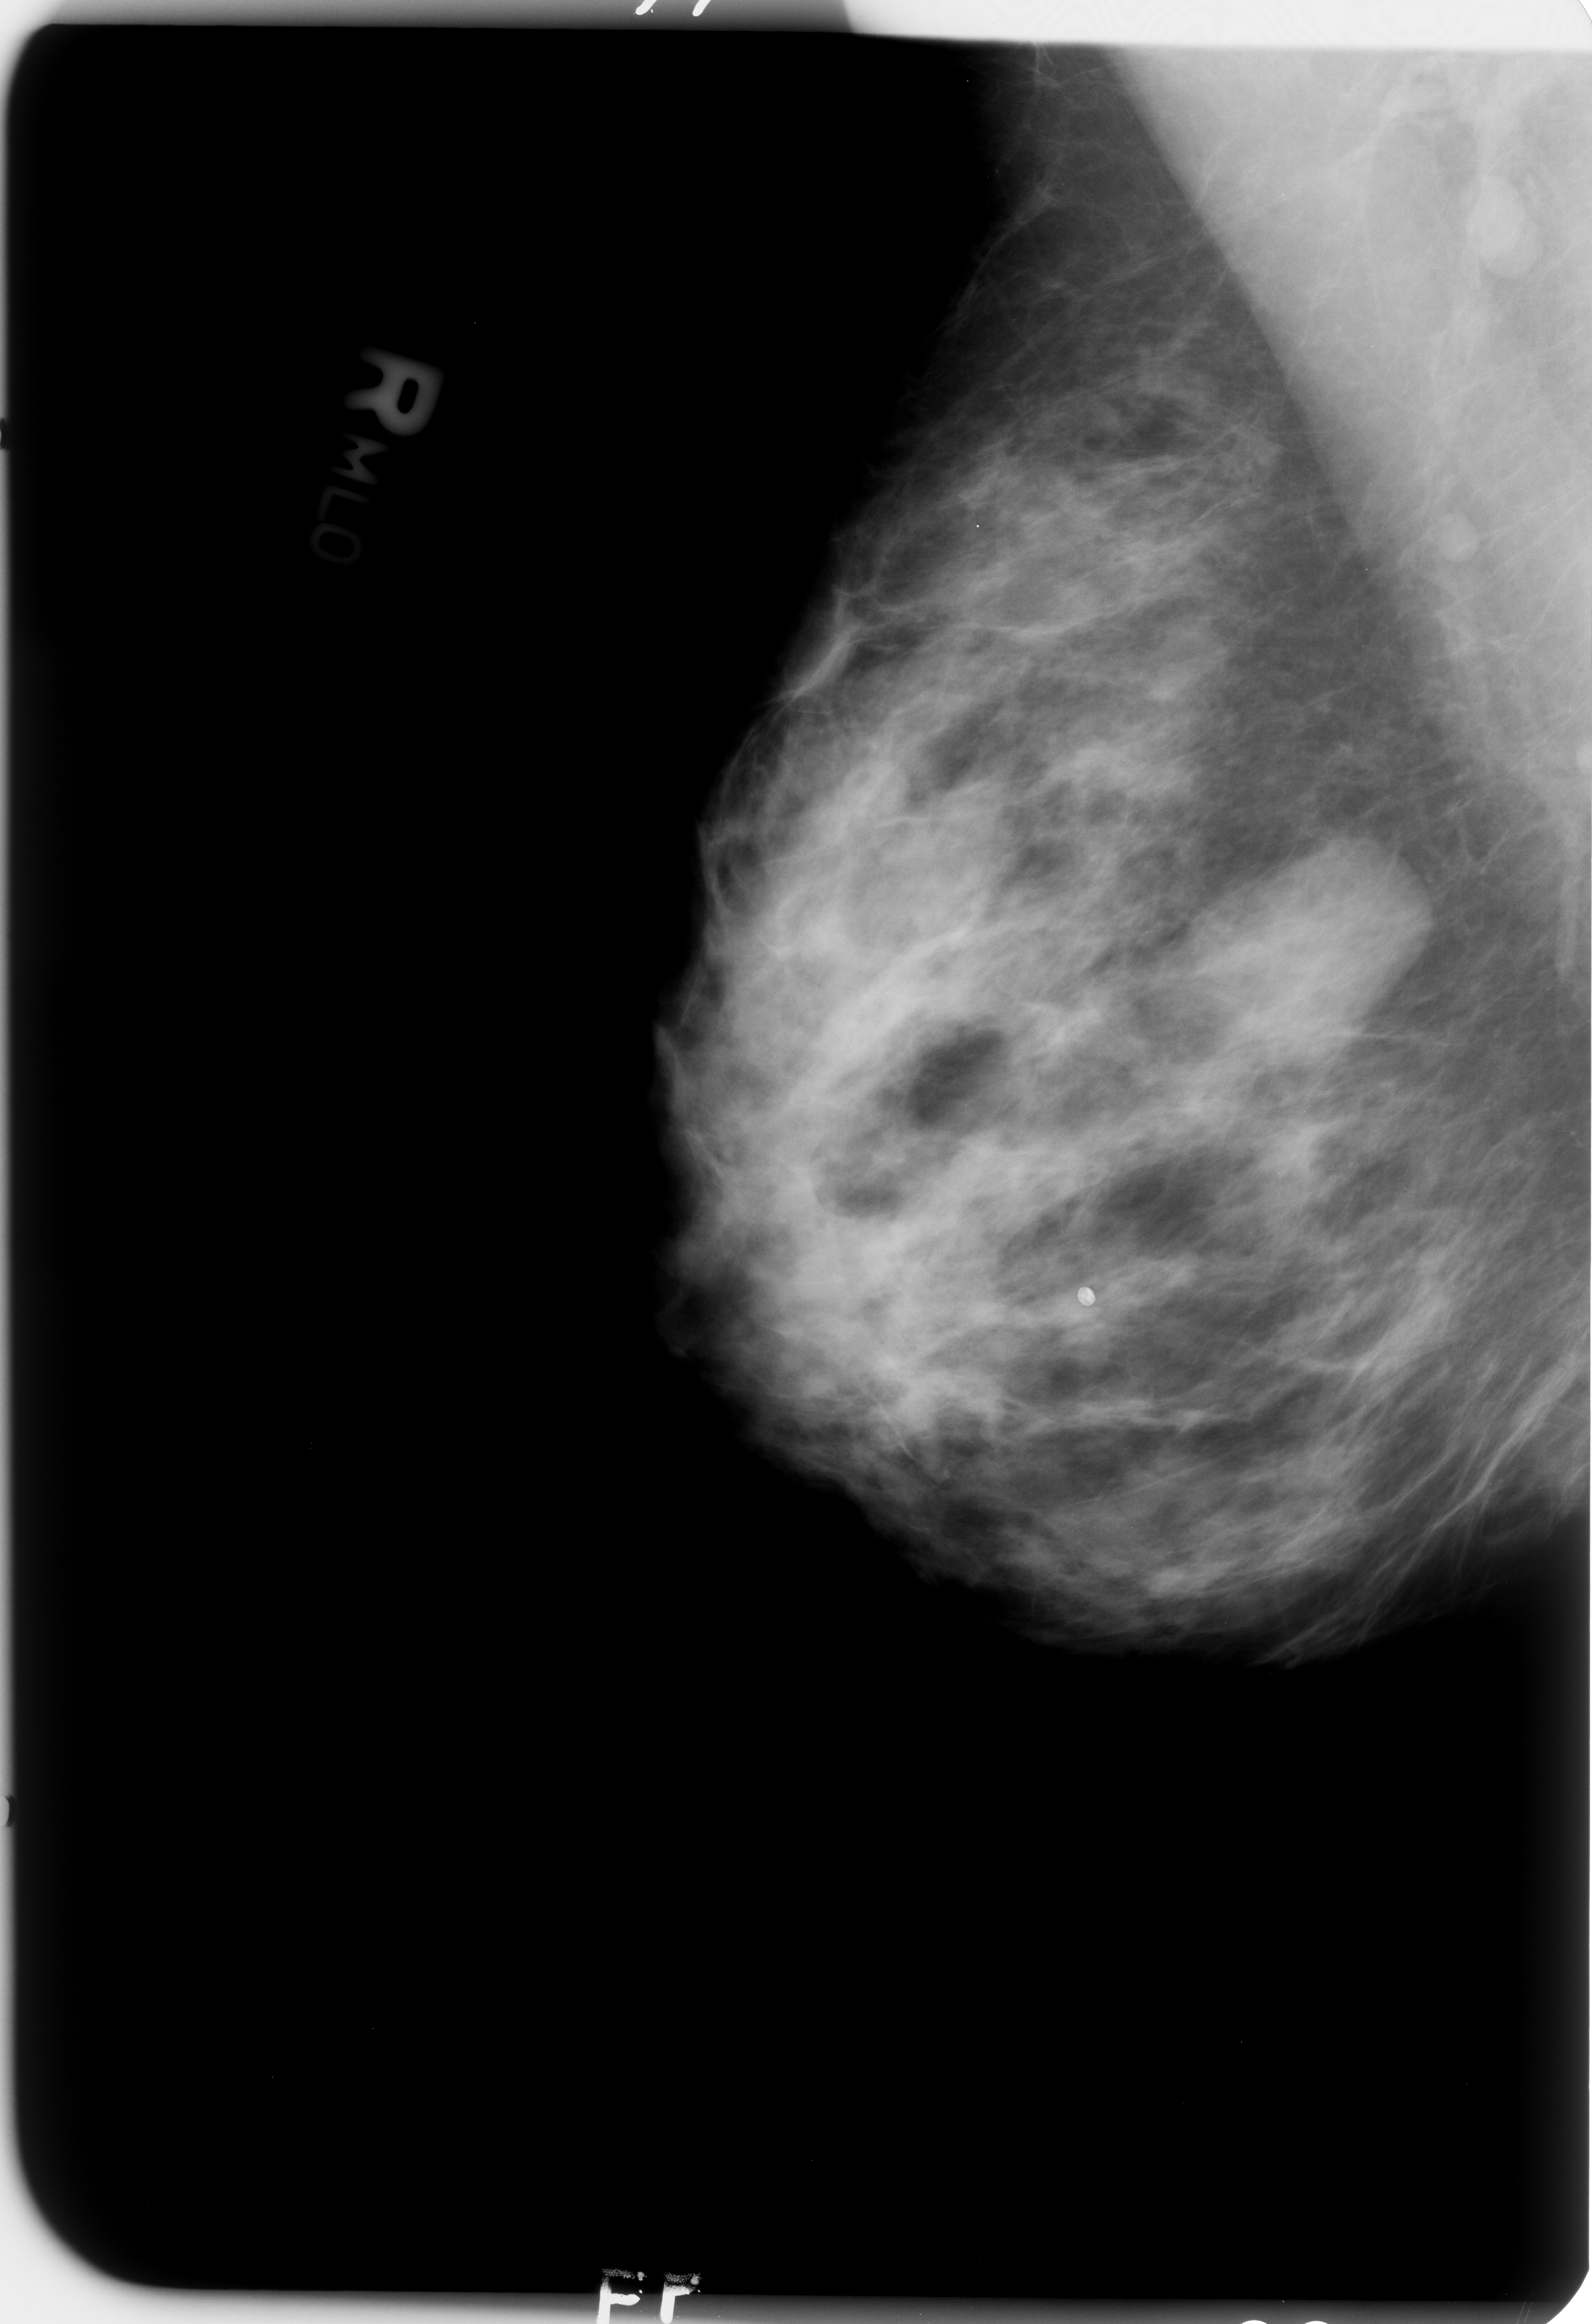
Mammogram (digitized film); right breast; MLO view; 1592 × 2324 image matrix.
Expert-marked regions of interest on this film, with their recorded descriptors:
- mass, shape oval, margins circumscribed / obscured; BI-RADS assessment category 3; subtlety rating 4 on a 1 (subtle) to 5 (obvious) scale; pathology result (as recorded, not read from the image): benign: box from (x=1173, y=824) to (x=1436, y=1047) px